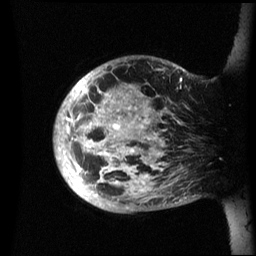
Breast MRI (dynamic contrast-enhanced), one sagittal slice. Slice 10 of 60 in the series (ordered by position). Dynamic contrast-enhanced series, image 2 of 3 at this slice position (ordered by acquisition). 1.5 T. TE 4.2 ms, TR 8.4 ms. 2.4 mm slice thickness. 256 × 256 image matrix, field of view 230 × 230 mm. Patient: female, 48 years.
Structures marked on this image (semi-automatic segmentation, software-assisted and operator-edited):
- analysis volume of interest (the breast-tissue region the enhancement analysis was run in; not a lesion): bounding box (x1, y1, x2, y2) in pixels: (54, 56, 195, 213)
- tumour enhancement mask (voxels above the 70 % enhancement threshold inside the analysis volume of interest): (54, 73, 182, 197)